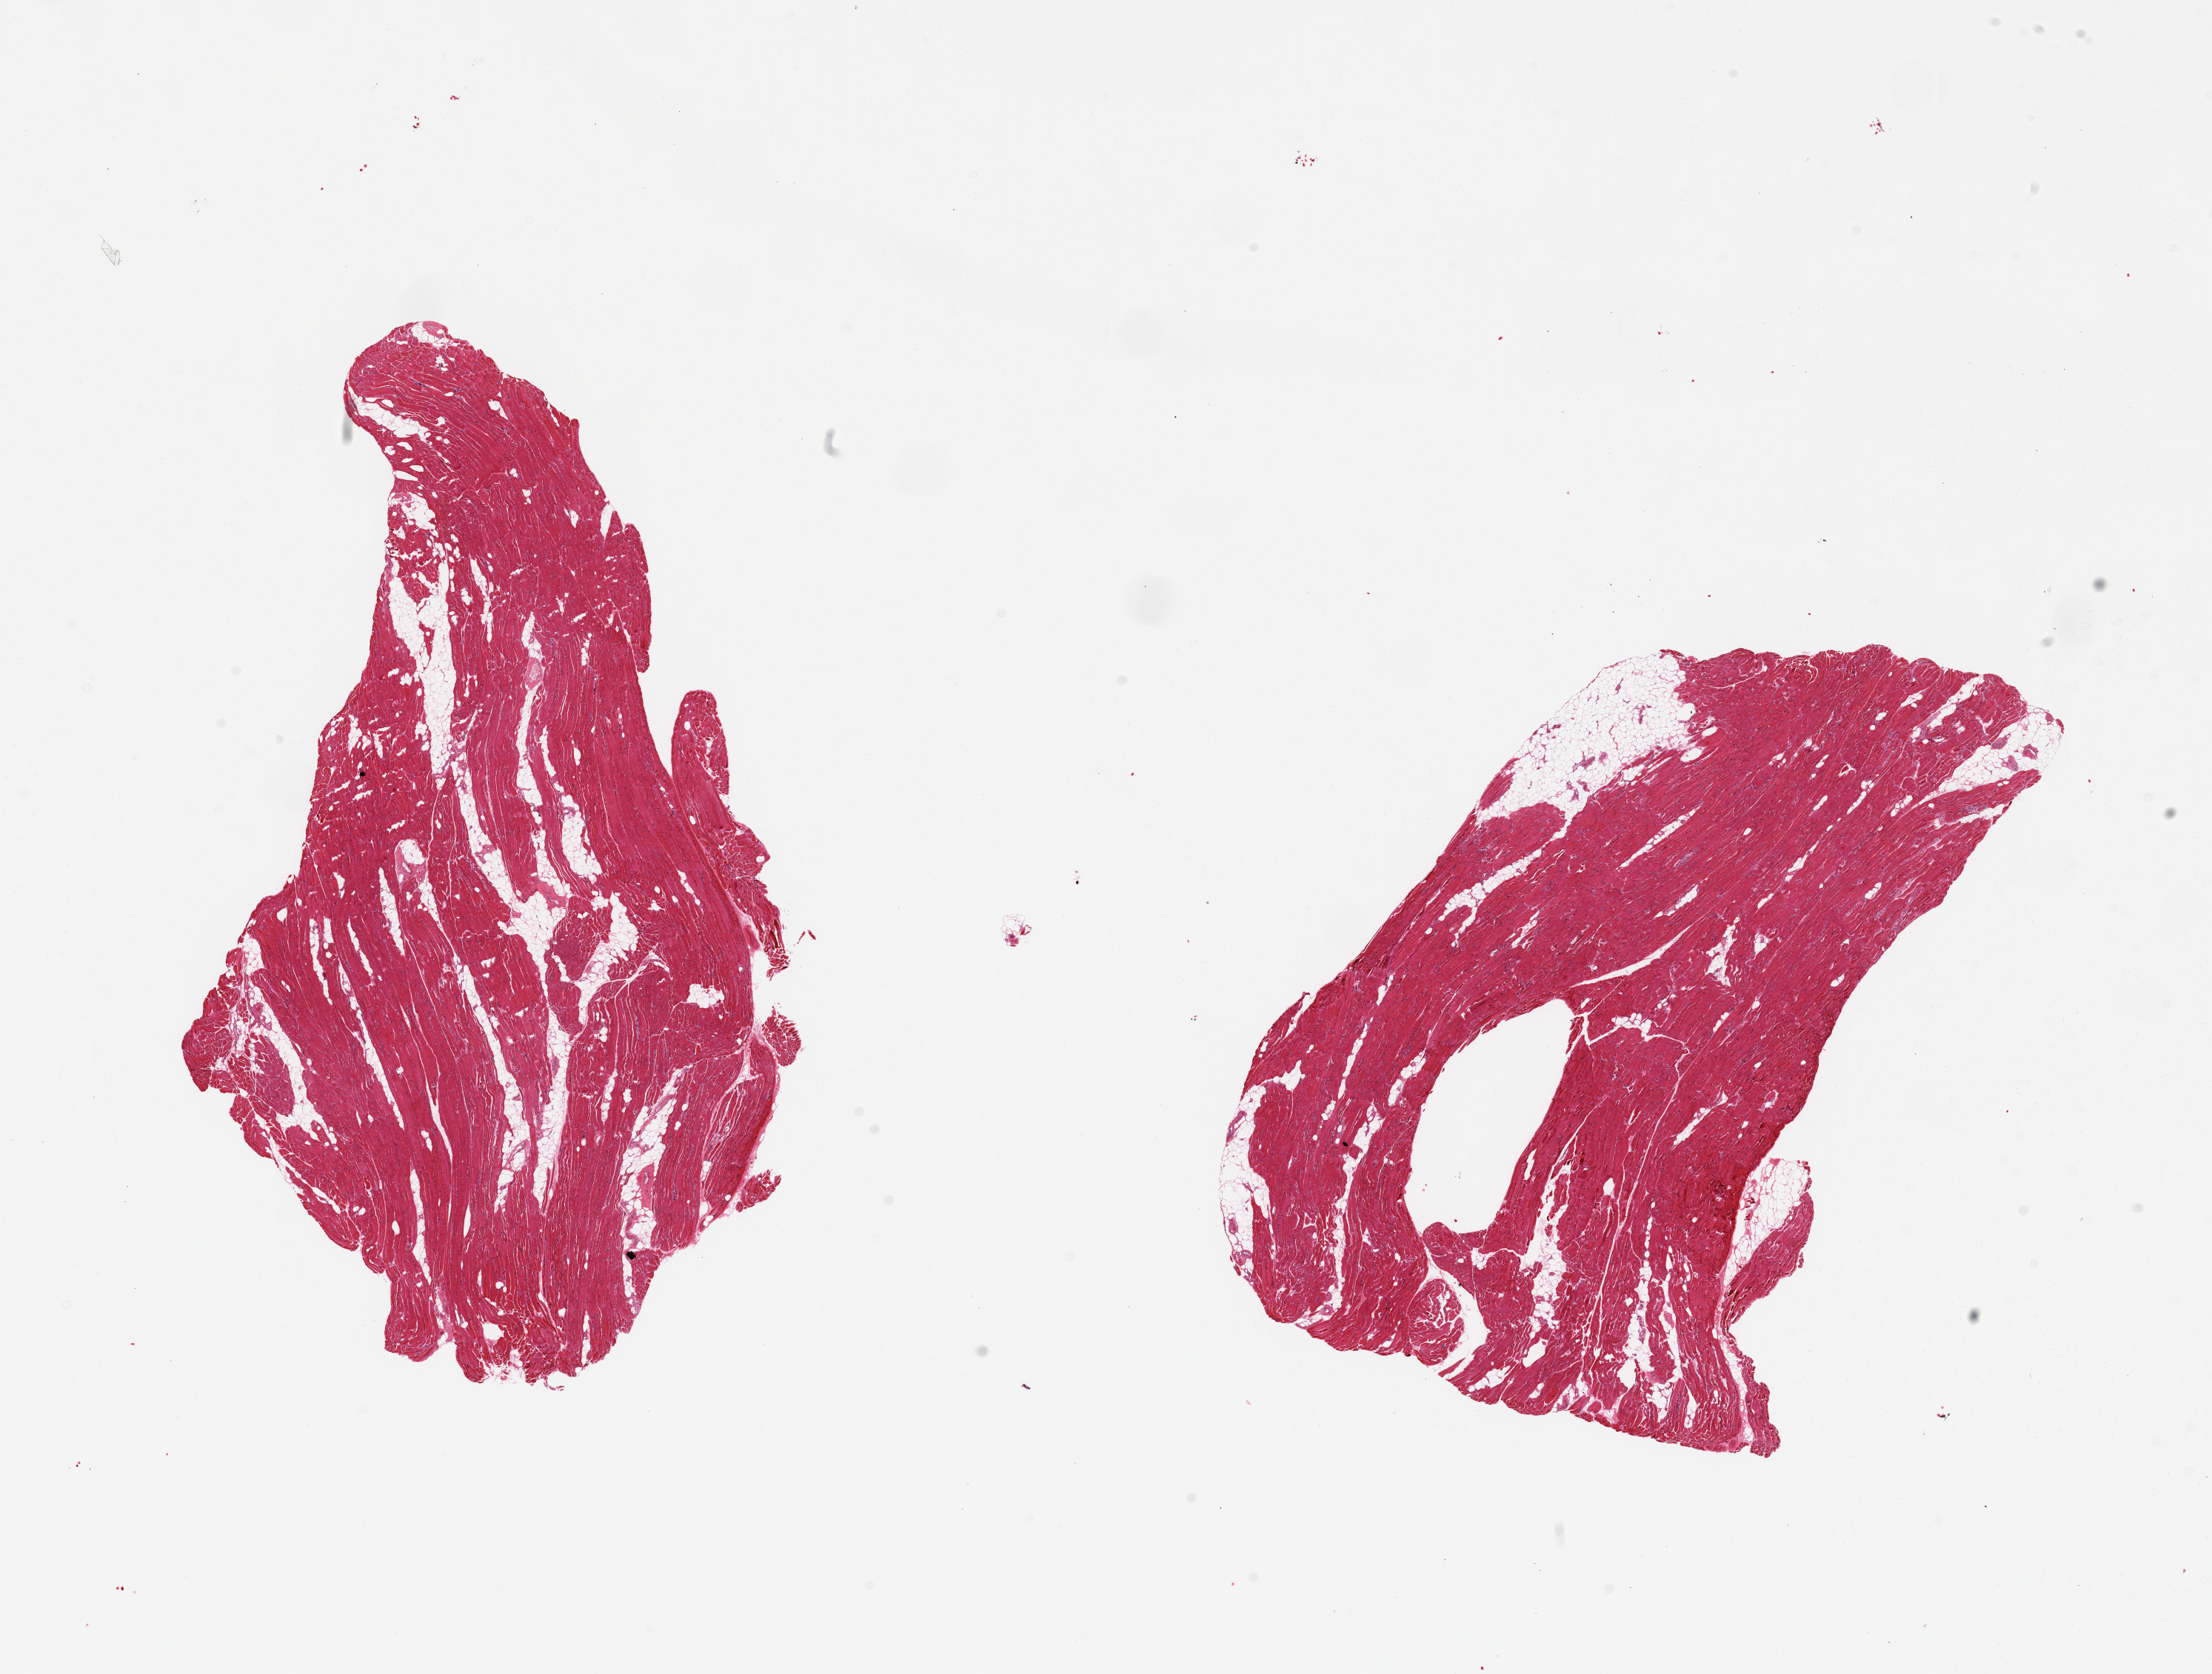
Digitized haematoxylin and eosin-stained section, brightfield, a low-resolution overview of the entire scanned area, about 23.6 x 17.9 mm (from a 20x scan), PAXgene-fixed, paraffin-embedded tissue, sampled site (target tissue): skeletal muscle, tissue donor sample. Female donor.
* review note (as recorded): 2 pieces; 10-20% internal fat